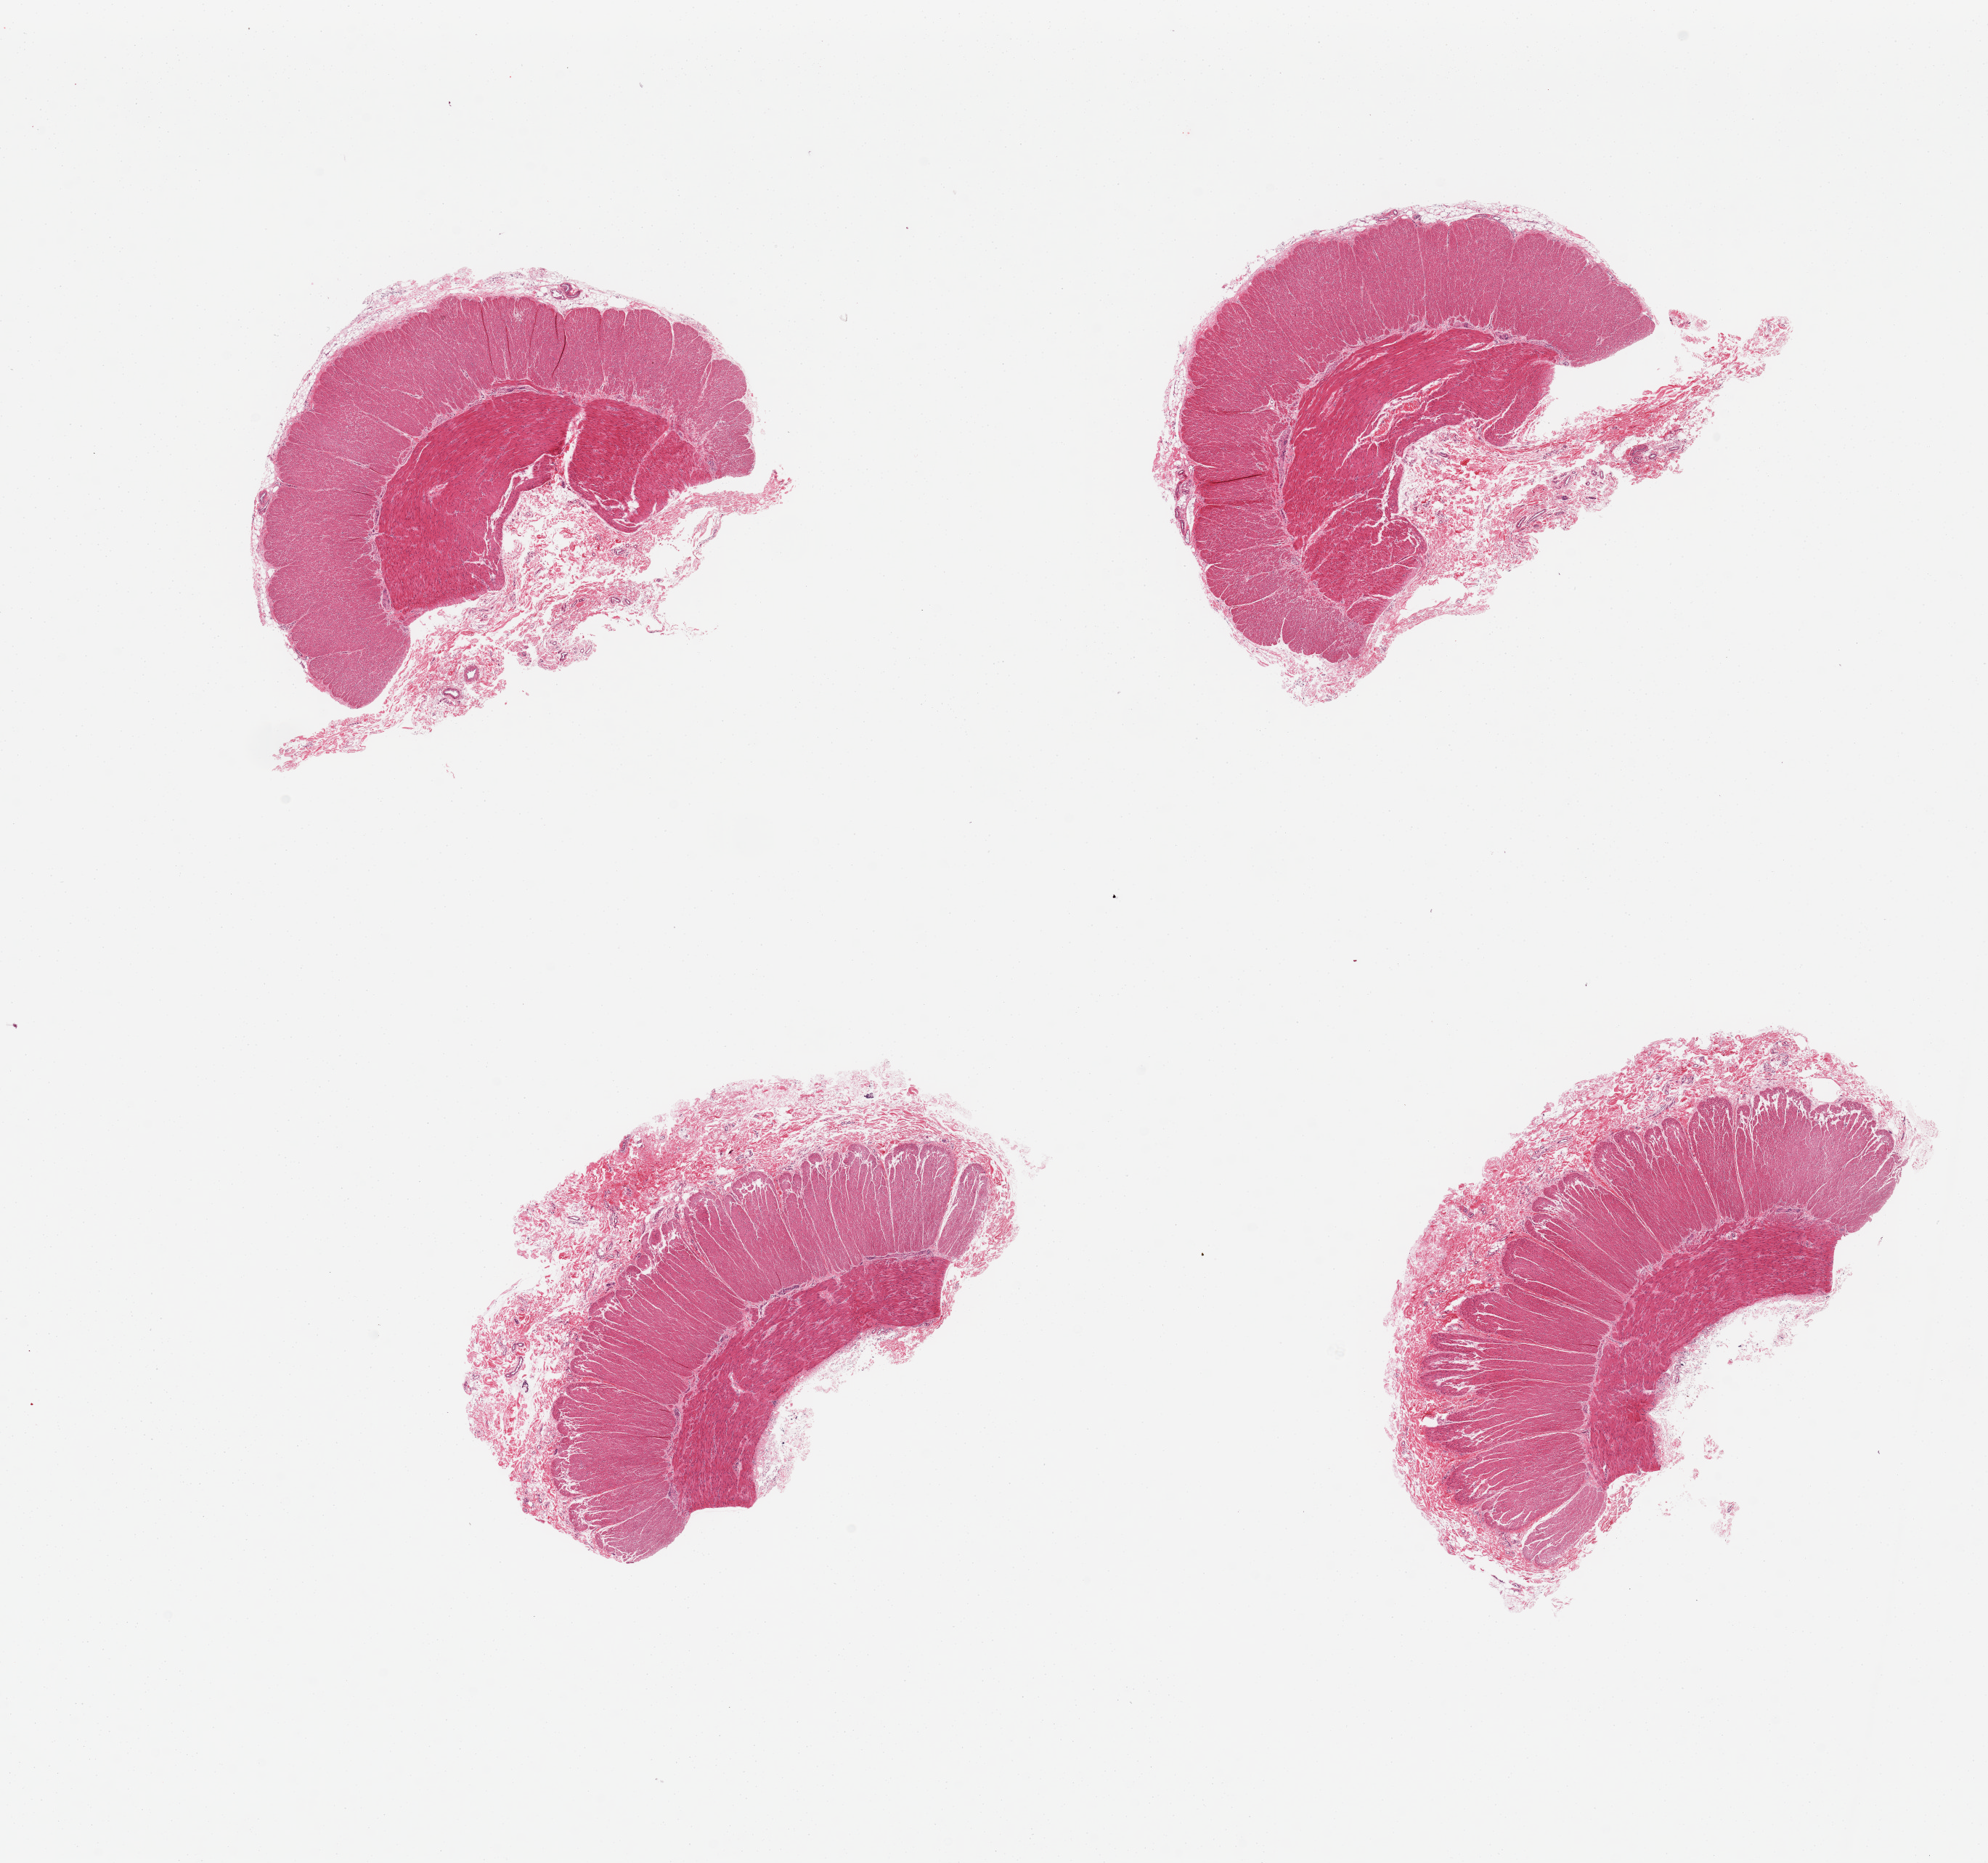
Digitized hematoxylin and eosin (H&E)-stained section — low-resolution overview of the scanned area, about 21.7 x 20.3 mm, PAXgene-fixed, paraffin-embedded tissue, target tissue: transverse colon, donor tissue sample.
Review note (as recorded): 4 pieces, muscularis only.